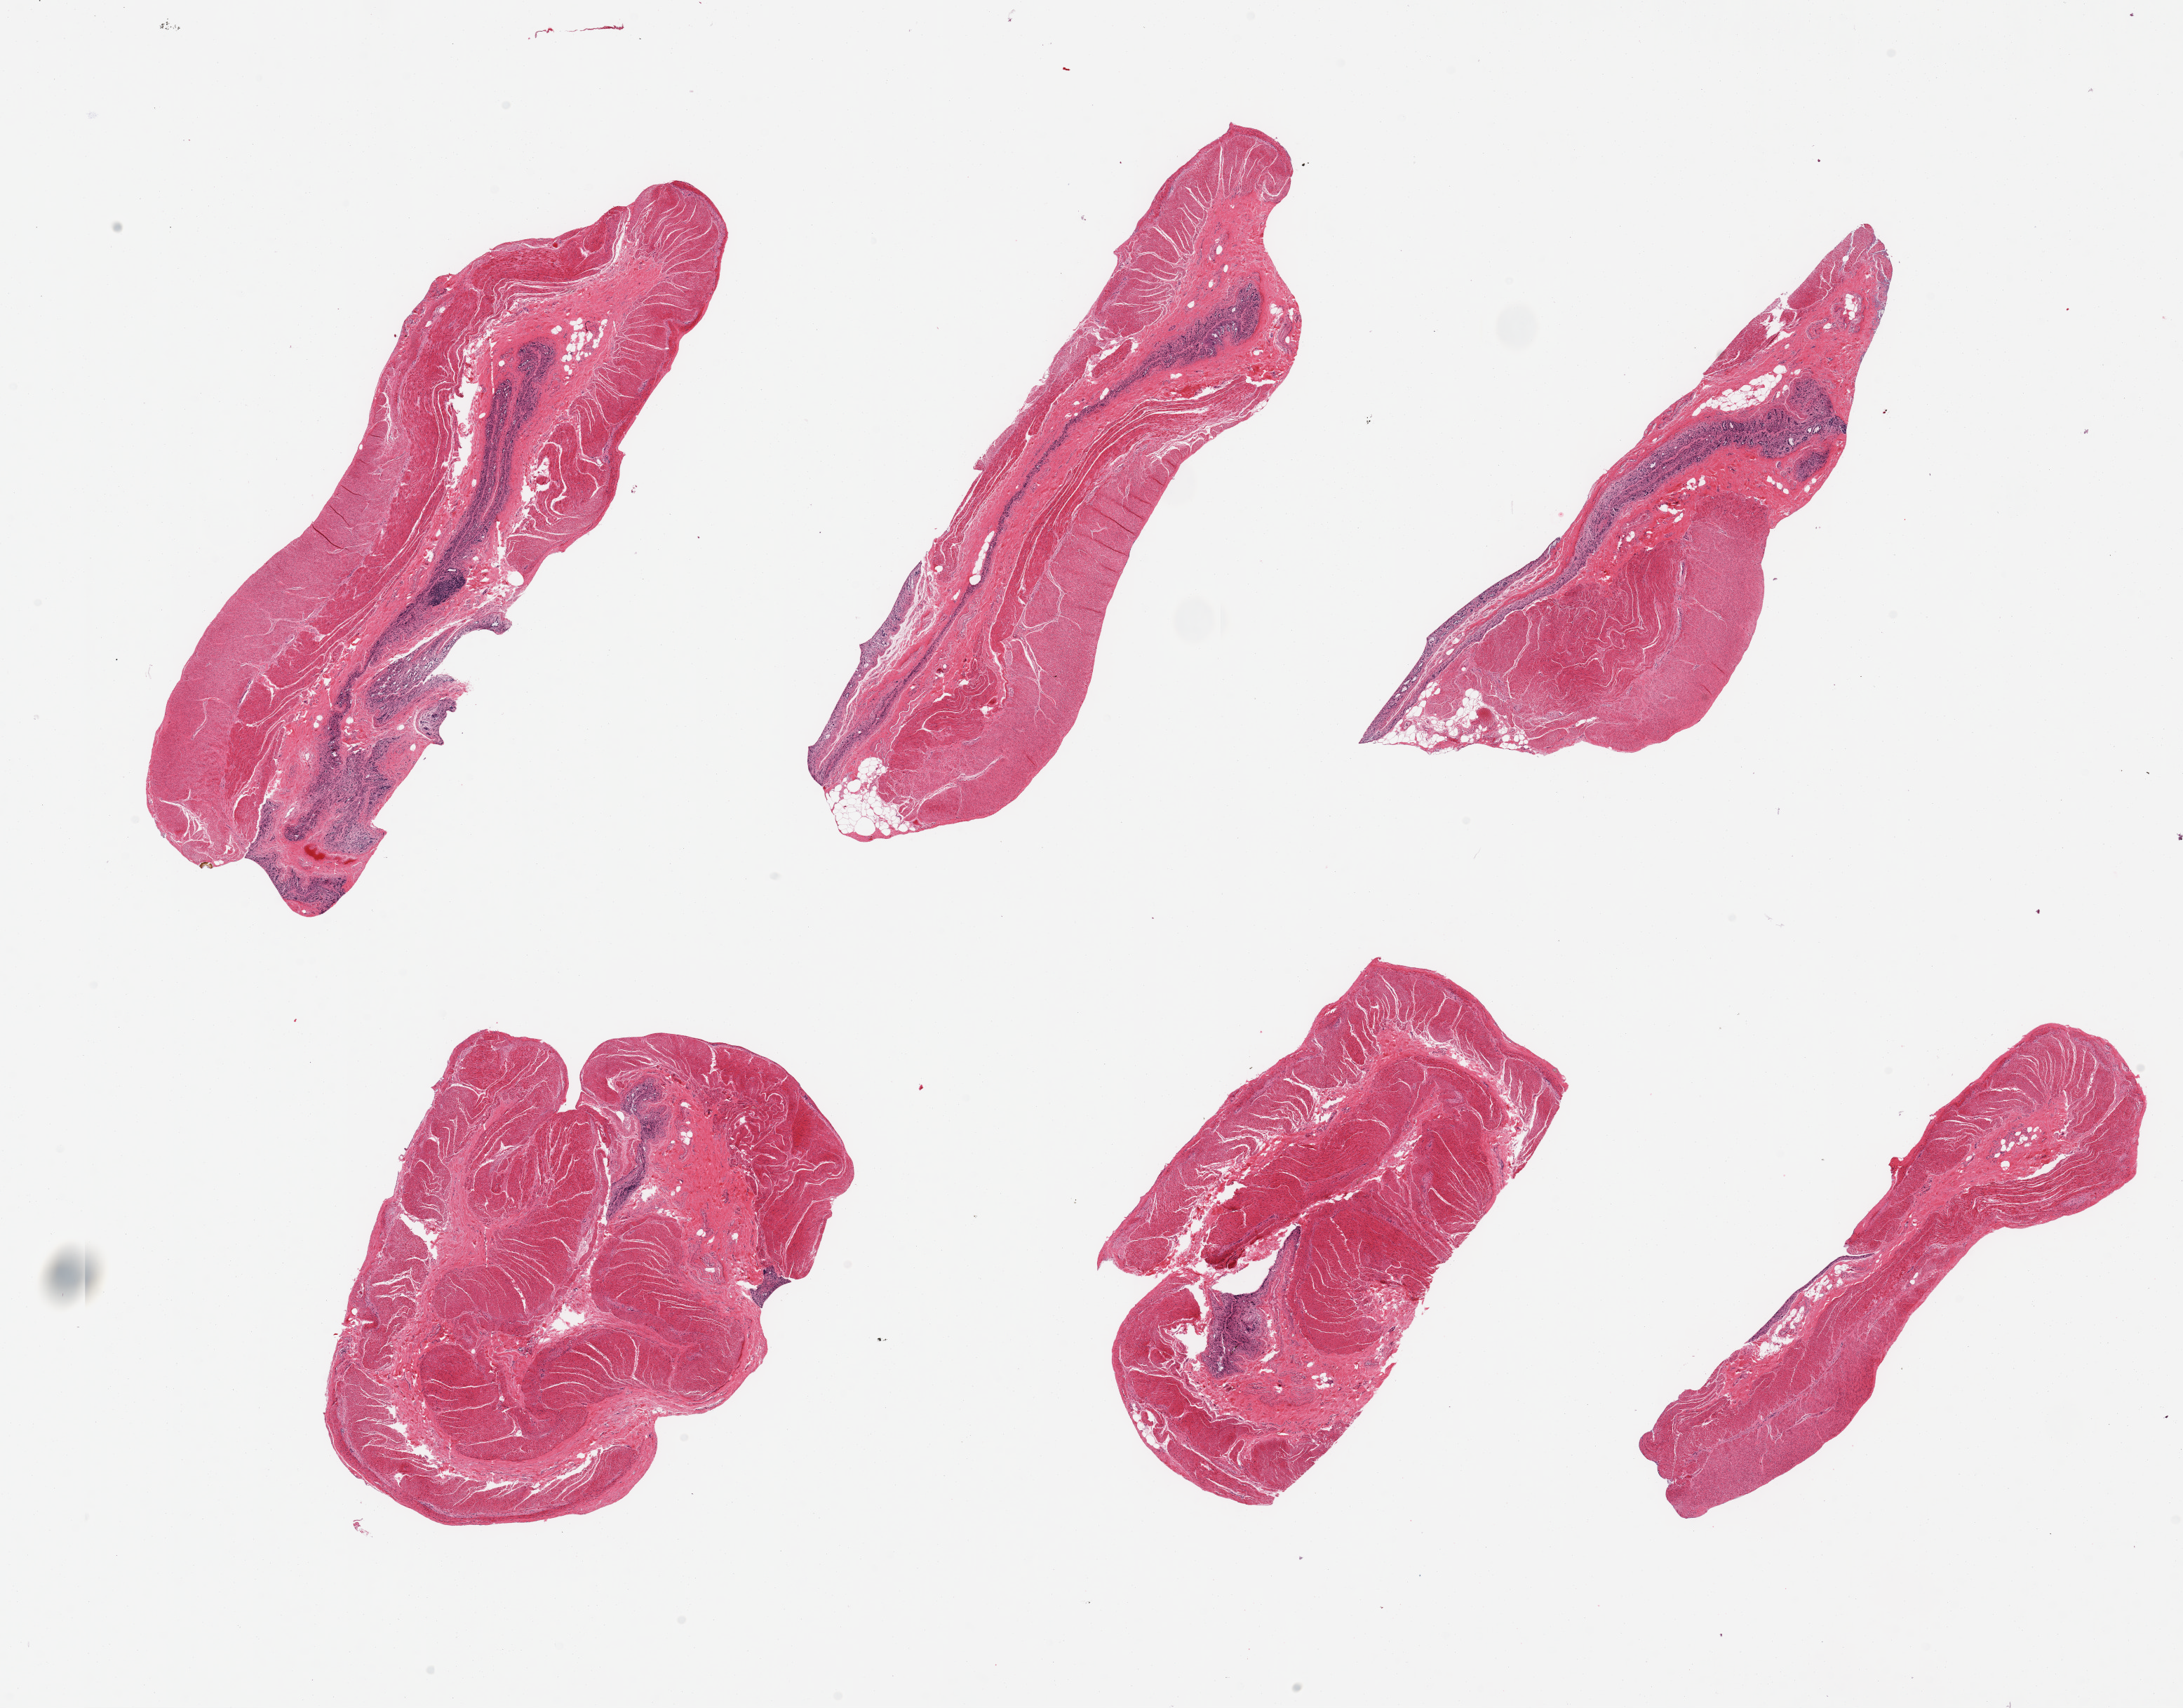
H&E whole-slide image, shown as a low-resolution overview of the whole scanned area (about 24.6 x 19.3 mm, slide scanned at 20x). PAXgene-fixed paraffin-embedded (PFPE) section. Sampled site (target tissue): transverse colon. Tissue donor sample. Male donor.
- review note (as recorded): 6 pieces, target mucusa with advanced autolysis, largely sloughed